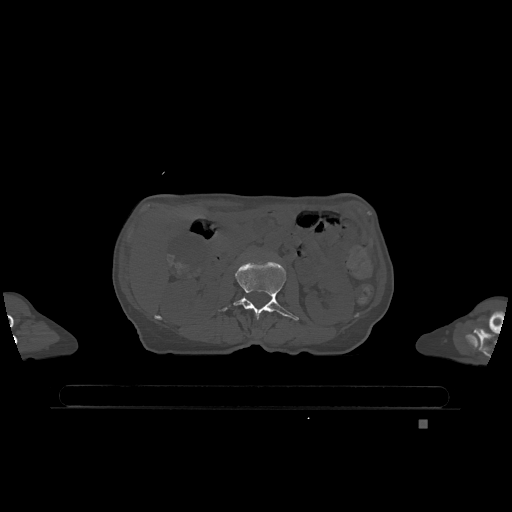
CT including the spine, one axial slice. Position 414 of 1317 along the scan axis. Bone window (W 1800 / L 400 HU). 0.5 mm slice thickness. 512 × 512 image matrix, field of view 500 × 500 mm. Patient: female, 74 years. From the clinical record (not read from this slice): primary cancer: lung; vertebrae with lytic lesions (as recorded): T1, T4, T5, T6, L4, L5.
Outlined on this slice (semi-automatic segmentation, software-assisted and operator-edited):
- L2 vertebra: bounding box [x1, y1, x2, y2] px = [218, 261, 299, 321]